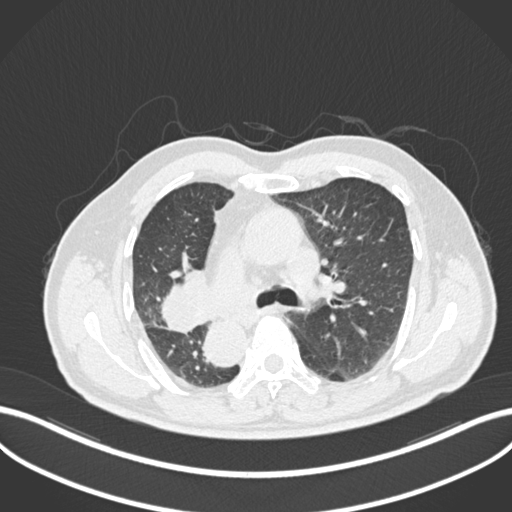
Chest CT, one axial slice. Reconstruction kernel B30f. Lung window (W 1500 / L -600 HU). 512 × 512 image matrix. Male patient, age 67 years. From the clinical record (not read from this slice): clinical TNM (as recorded): T2a N0 M0.
Outlined on this slice (rectangle marked by the reading radiologist):
- lung tumour (recorded histology: squamous cell carcinoma): bounding box <156,264,212,336> (left, top, right, bottom; pixels)